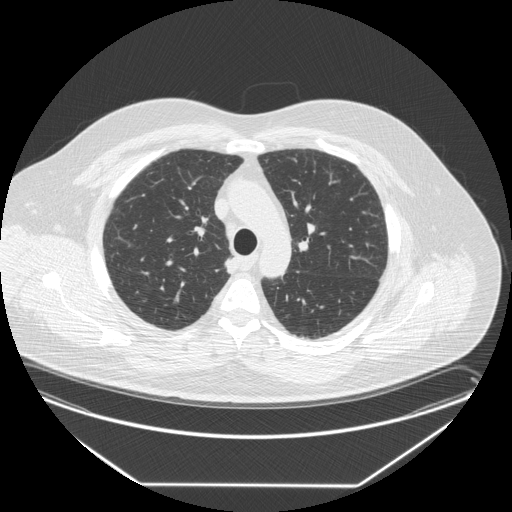
Axial slice from a low-dose chest CT screening exam; third annual screen; lung window (W 1500 / L -600 HU); 2.5 mm slice thickness; standard (soft-tissue) reconstruction kernel (STANDARD); 512 × 512 image matrix, field of view 440 × 440 mm. Male participant, aged 58 years at enrolment. Former smoker at enrolment.
• Lesion marked by an expert reader, bounding box [x1, y1, x2, y2] px = [210, 253, 240, 277].
• Reader record for this screening exam (exam-level; its link to the box is not recorded): non-calcified nodule or mass ≥4 mm, right upper lobe, 15 × 12 mm, smooth margins, soft tissue attenuation, pre-existing on the prior screen: no.
• Official screen result: positive, other.
• Later outcome: lung cancer diagnosed 17 days after this screen — large cell carcinoma, NOS, right upper lobe, stage IV (AJCC 6th edition), 35 mm at pathology.